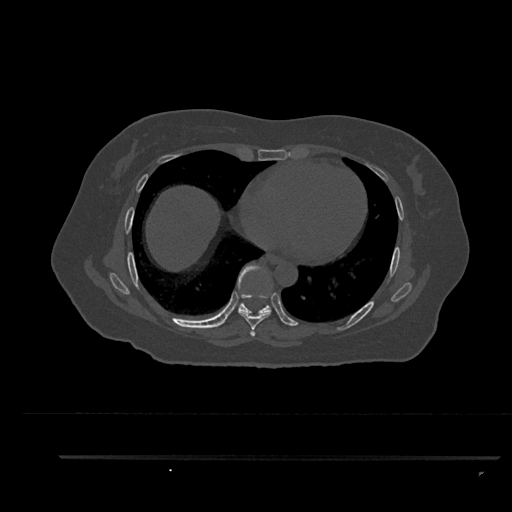
CT including the spine, one axial slice; slice 488 of 797 in the series (ordered by position); 120 kVp; bone window (W 1800 / L 400 HU); 0.5 mm slice thickness; 512 × 512 image matrix, field of view 408 × 408 mm. Female patient, age 44 years. Case-level facts recorded for this patient, not image findings: primary cancer: renal; vertebrae with lytic lesions (as recorded): L1.
Outlined on this slice (semi-automatic segmentation, software-assisted and operator-edited):
- T6 vertebra: box from (x=251, y=333) to (x=254, y=335) px
- T7 vertebra: (x=238, y=310)–(x=271, y=337)
- T8 vertebra: (x=237, y=264)–(x=272, y=316)